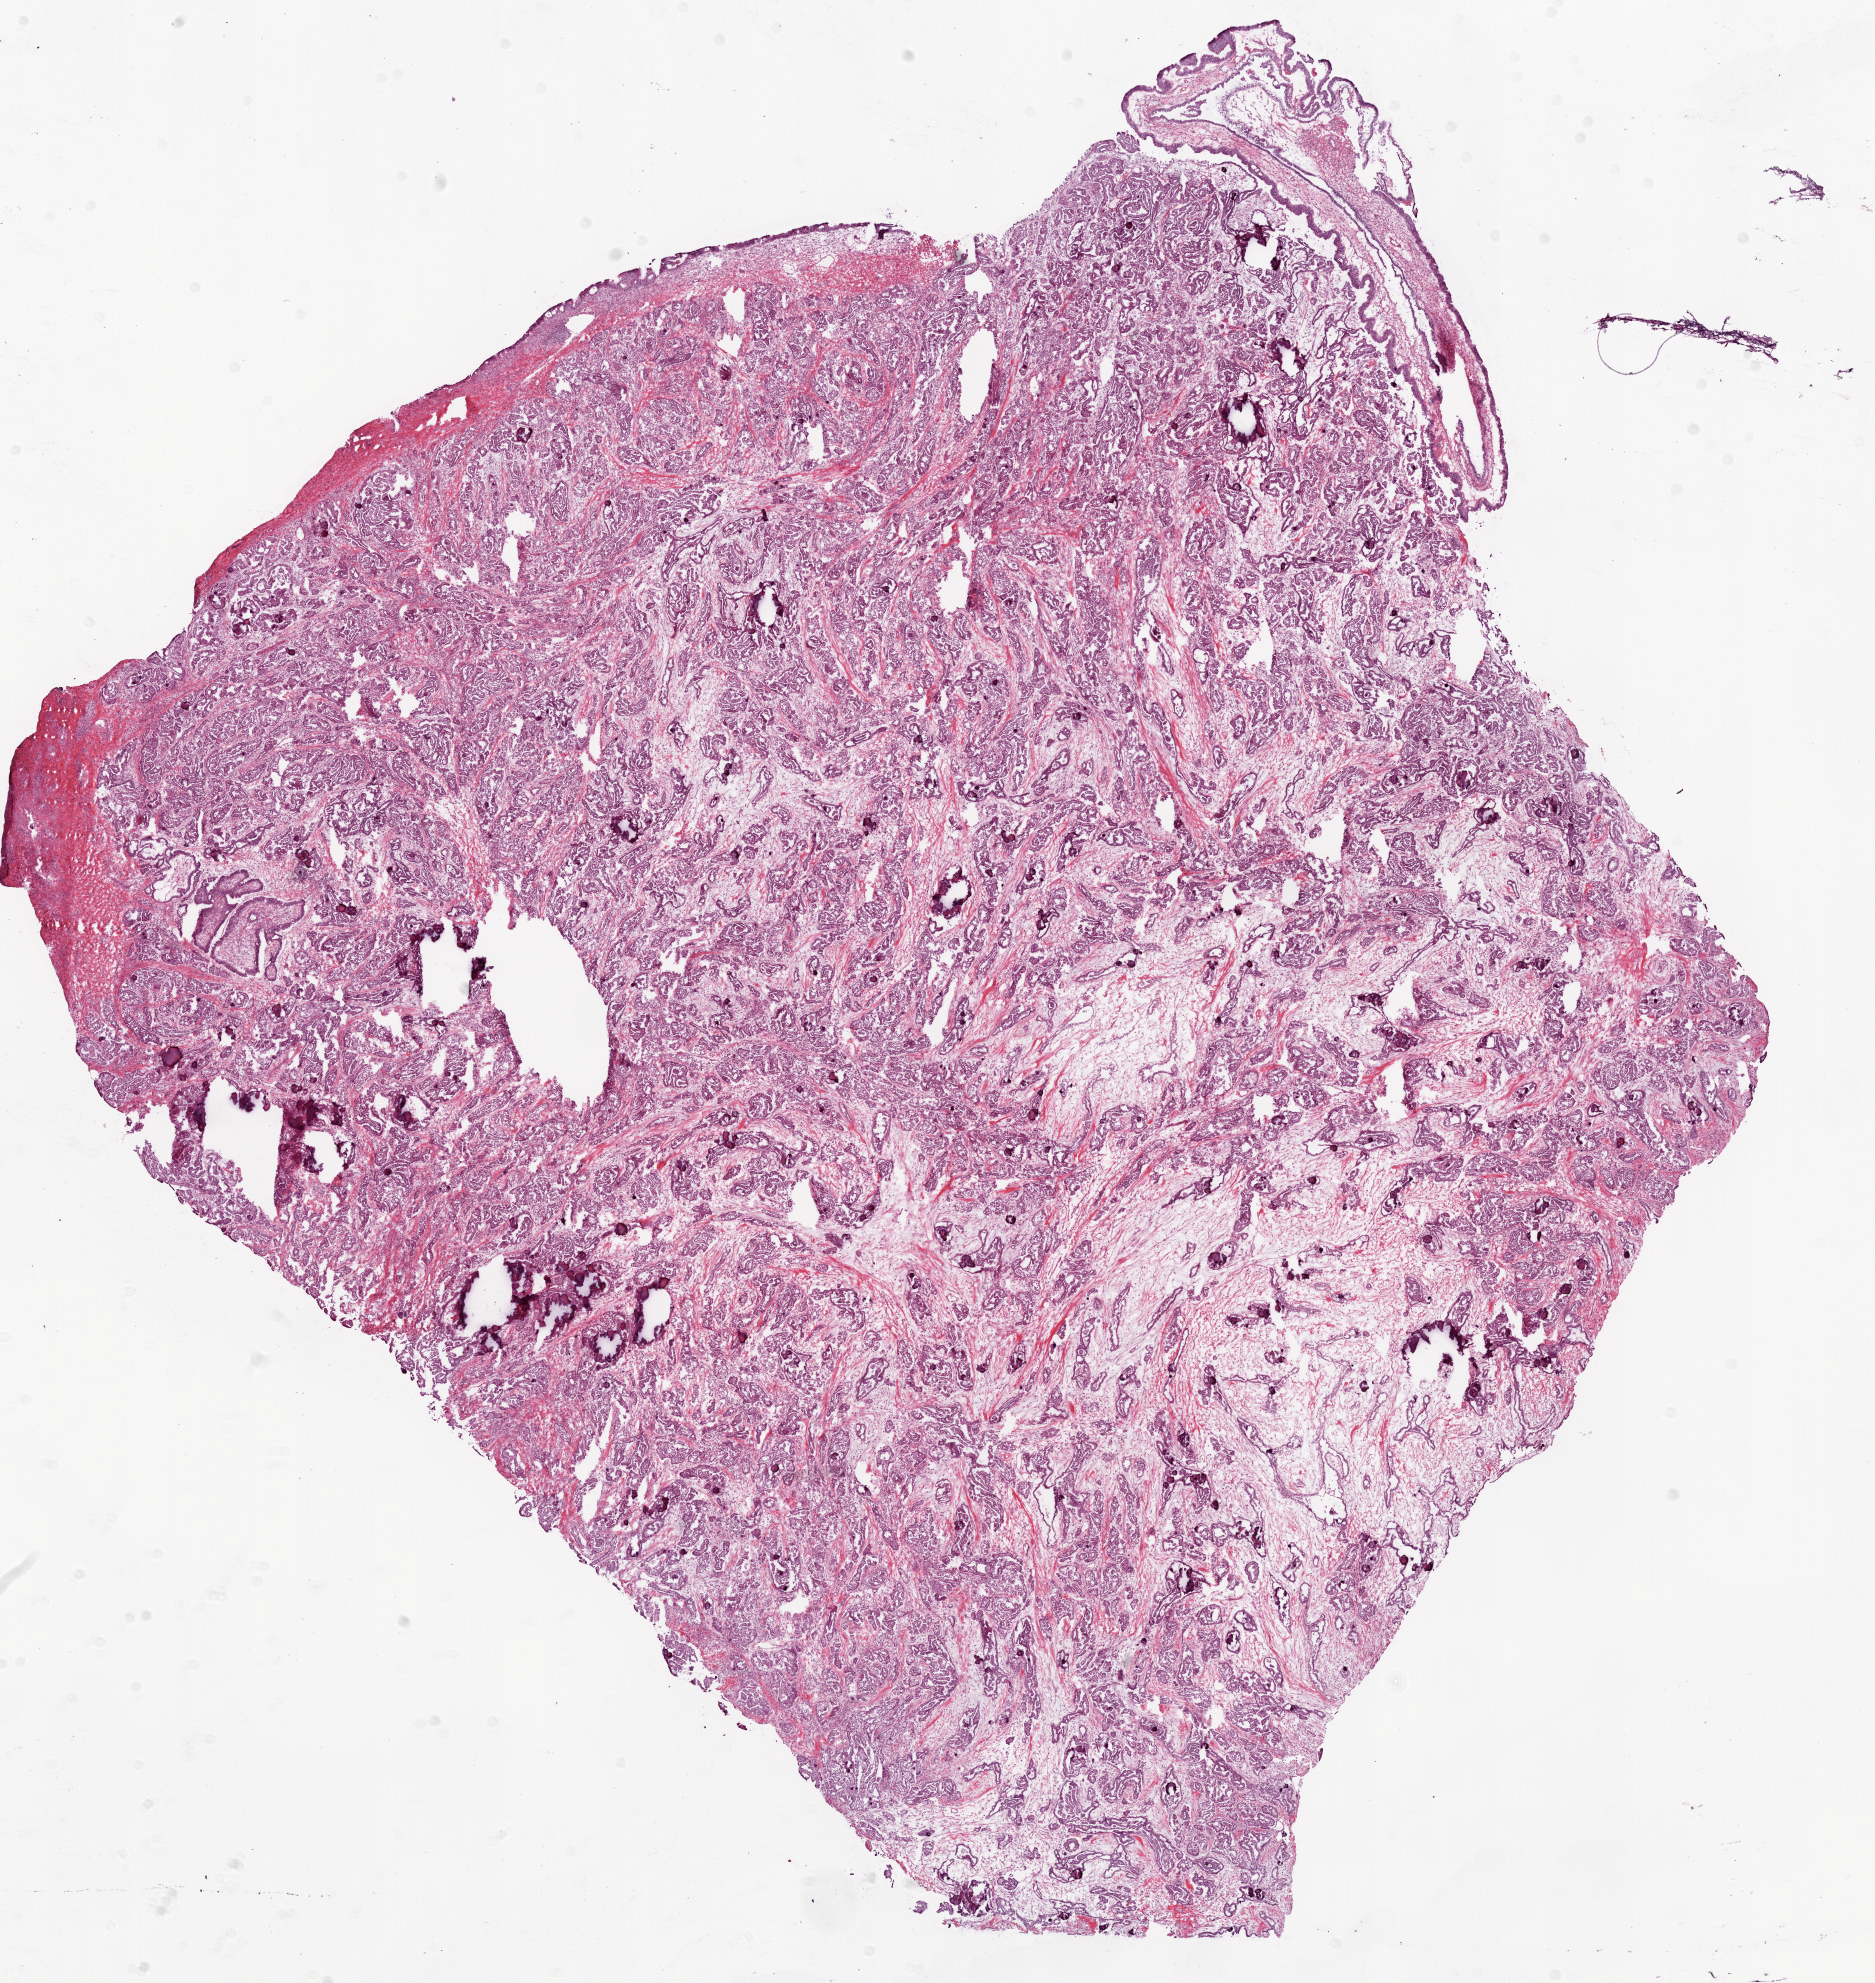
Whole-slide histology image, H&E, whole scanned area (about 15.0 x 15.9 mm) shown as a low-resolution overview; frozen section from the bottom of the tissue portion; primary tumour sample from the ovary. Patient: female, age at initial diagnosis 66 years. Histologic grade: G2 (moderately differentiated). Composition of this section per pathologist review: tumour cells 100%, tumour nuclei 90%, normal cells 0%, stromal cells 0%, necrosis 0%.
FIGO stage: IIIC. Laterality: bilateral. Histologic diagnosis: Serous cystadenocarcinoma, NOS.